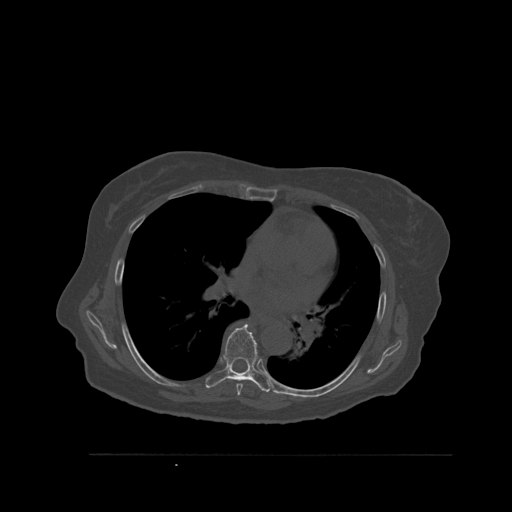
CT including the spine, one axial slice; slice 369 of 527 in the series (ordered by position); bone window (W 1800 / L 400 HU); 1.5 mm slice thickness; 512 × 512 image matrix. Patient: female, 73 years. From the clinical record (not read from this slice): primary cancer: breast; vertebrae with lytic lesions (as recorded): L2.
Annotated regions visible in this slice (semi-automatically segmented with operator editing):
- T6 vertebra: bounding box <236,384,243,396> (left, top, right, bottom; pixels)
- T7 vertebra: <205,324,271,393>